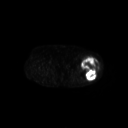
FDG PET of an extremity soft-tissue mass (from a PET/CT study), one axial slice; slice 231 of 267 in the series (ordered by position); 128 × 128 image matrix, field of view 700 × 700 mm. Female patient, age 62 years. From the clinical record (not read from this slice): histological type: undifferentiated – high grade; grade: high; site of the primary tumour: left thigh.
Structures marked on this image (expert contour drawn on MRI and transferred to this co-registered scan by the dataset authors):
- gross tumour volume including surrounding oedema: bounding box [x1, y1, x2, y2] px = [81, 56, 99, 80]
- gross tumour volume (mass): [81, 56, 99, 80]